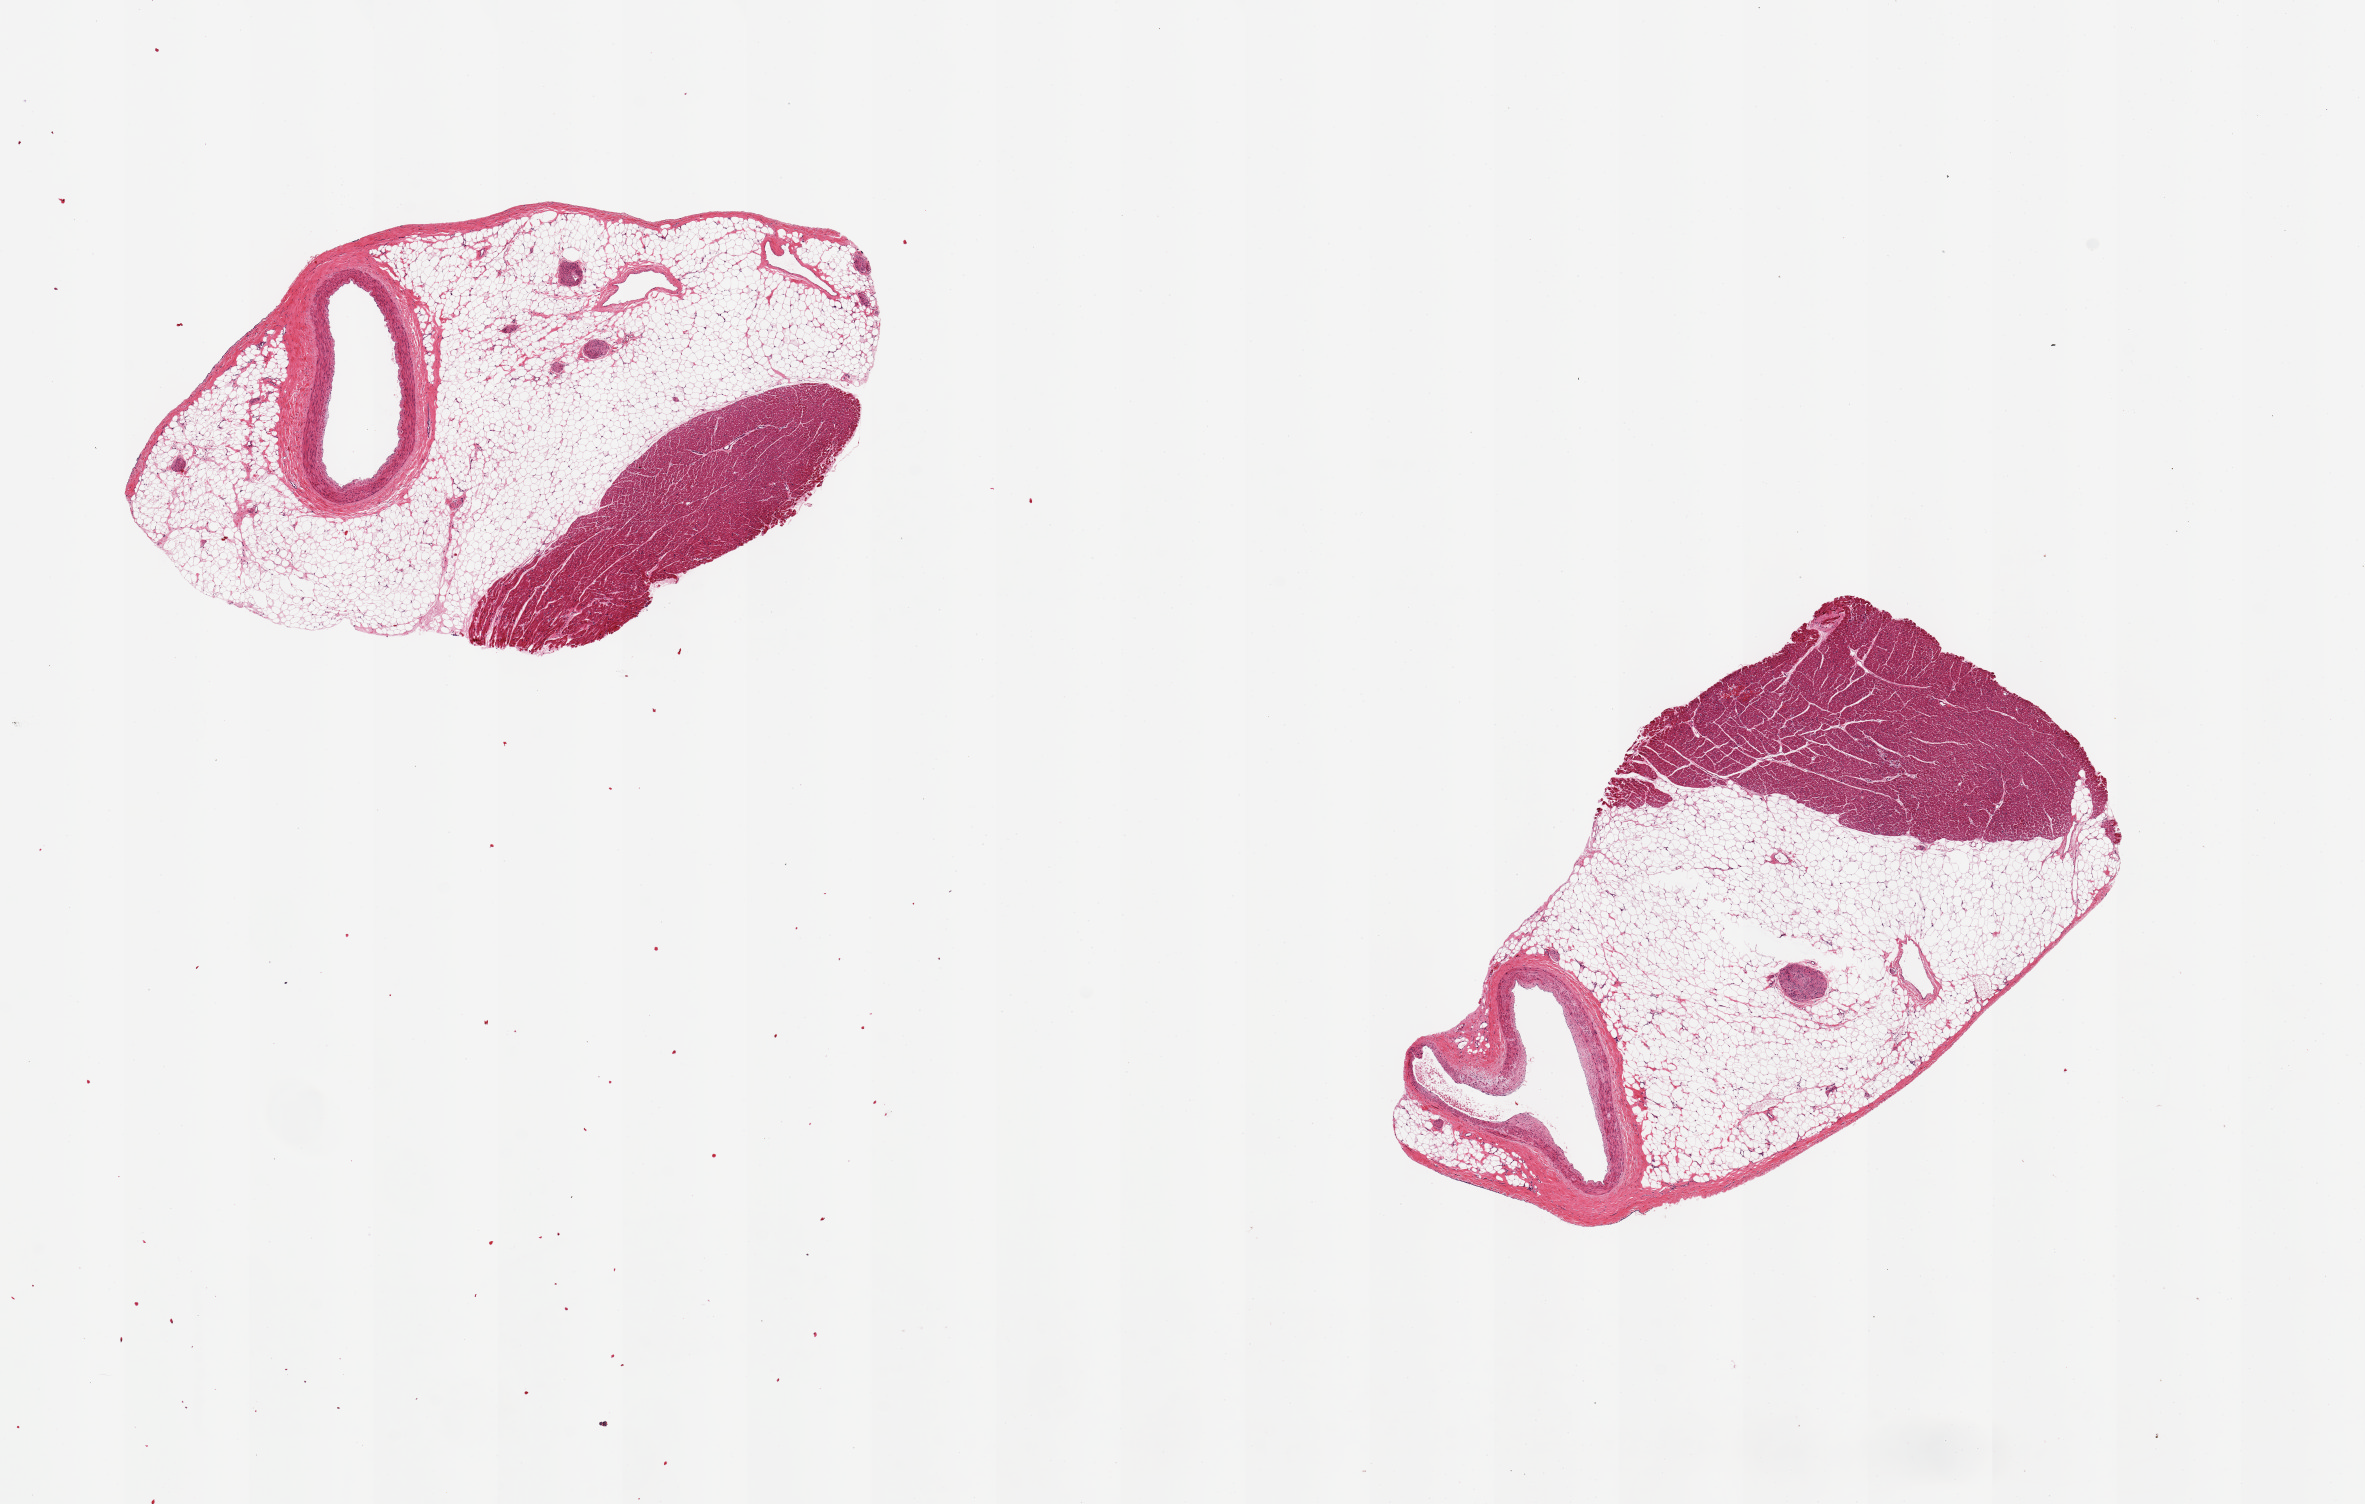
Whole-slide image, H&E stain, brightfield — shown as a low-resolution overview of the whole scanned area (about 18.7 x 11.9 mm, slide scanned at 20x); PAXgene-fixed paraffin-embedded (PFPE) section; section of coronary artery (target tissue); tissue donor sample. Female donor.
• reviewer comment on this tissue sample: 2 pieces, arteries 2x1mm make up about 15% of specimen with abundant pericardial fat and myocardium